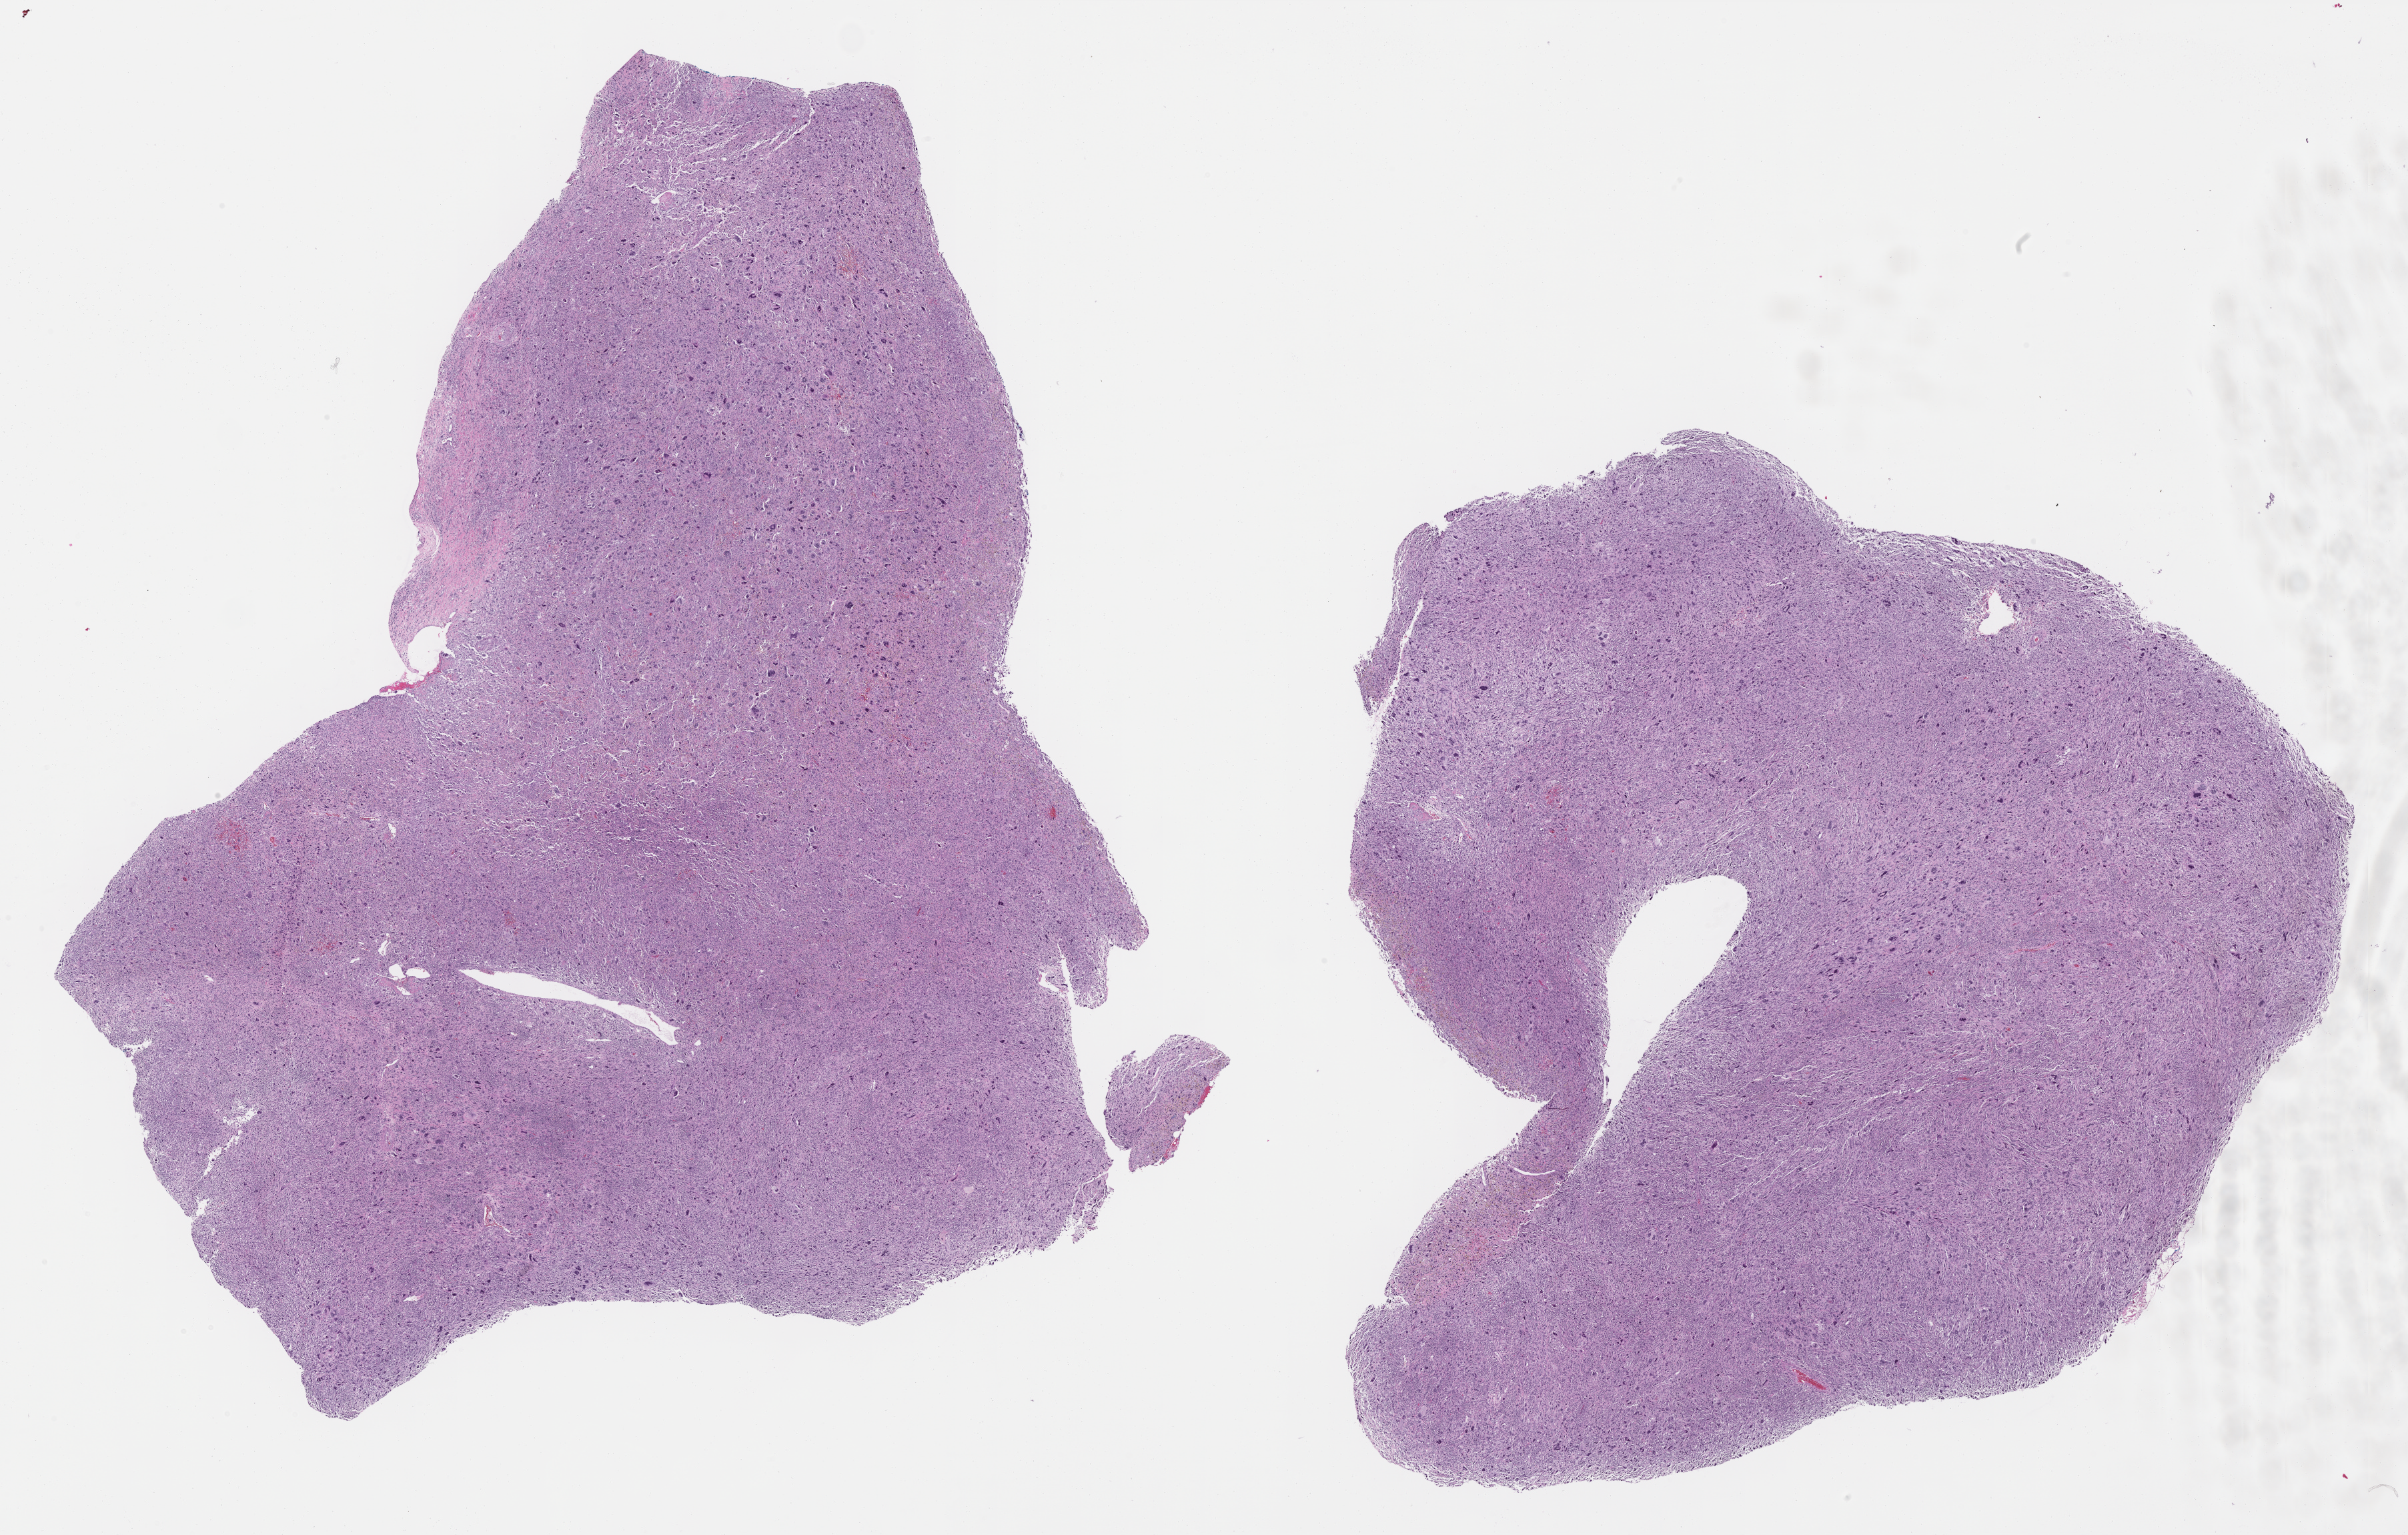
Digitized H&E-stained tissue section (whole slide) — low-resolution overview of the scanned area, about 29.0 x 18.5 mm, formalin-fixed paraffin-embedded (FFPE) diagnostic section, sample: primary tumour, connective, subcutaneous and other soft tissues. Male patient; age at initial diagnosis 71 years.
Pathologic diagnosis: Undifferentiated sarcoma (connective, subcutaneous and other soft tissues of trunk, NOS).